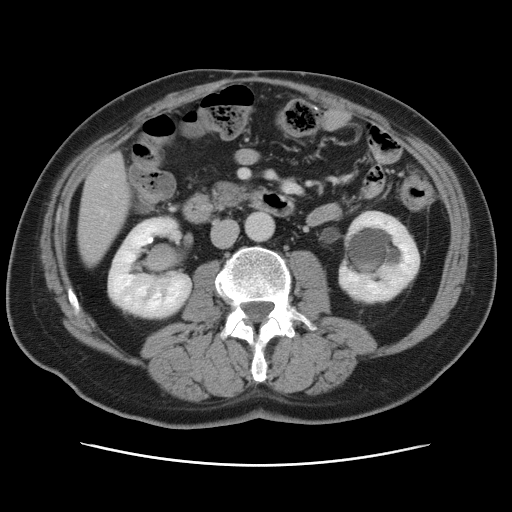
Contrast-enhanced abdominal CT, one axial slice; position 20 of 80 along the scan axis; intravenous contrast given; soft-tissue window (W 400 / L 40 HU); 5 mm slice thickness; 512 × 512 image matrix, field of view 370 × 370 mm. Male patient, age 69 years. Case-level facts recorded for this patient, not image findings: diagnosis: colorectal cancer liver metastases, imaged before liver resection; multiple liver metastases: no; largest metastasis: 5 cm; chemotherapy before resection: no.
Outlined on this slice (expert manual segmentation):
- liver: bounding box [x1, y1, x2, y2] px = [78, 154, 130, 263]
- planned liver remnant (the part of the liver to remain after resection): [78, 224, 118, 262]